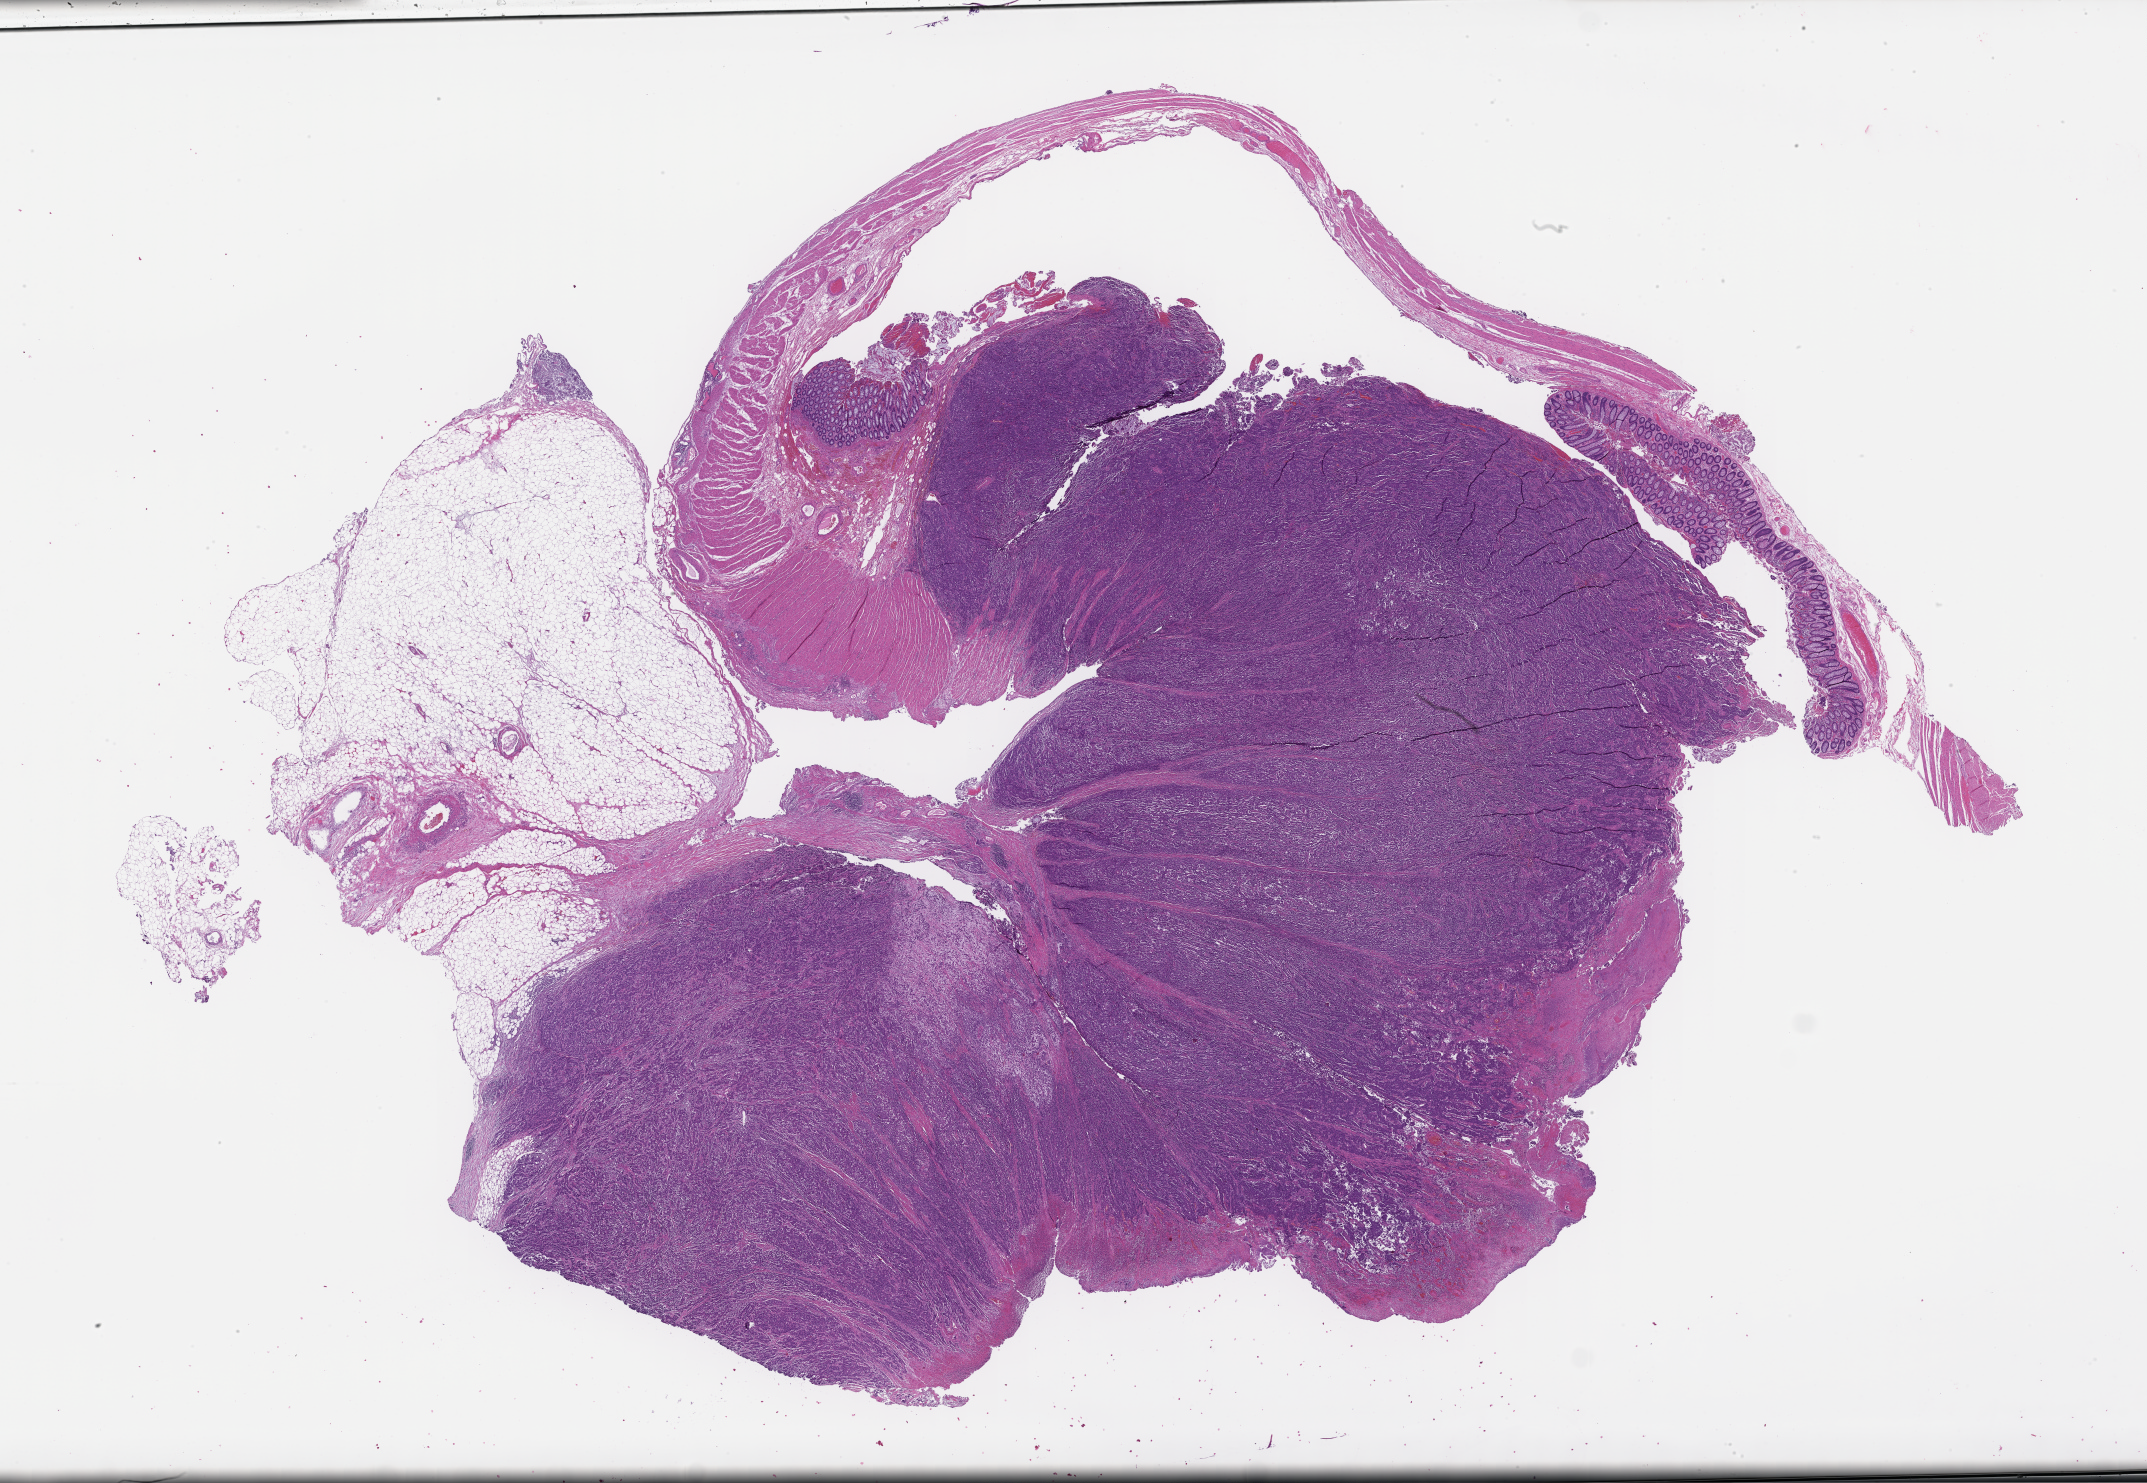
Hematoxylin and eosin (H&E) whole-slide image — shown as a low-resolution overview of the whole scanned area (about 34.7 x 24.0 mm); formalin-fixed, paraffin-embedded (FFPE) tissue; tissue site: colon. Patient sex: female.
This section: primary tumor. Diagnosis: Colorectal Carcinoma.